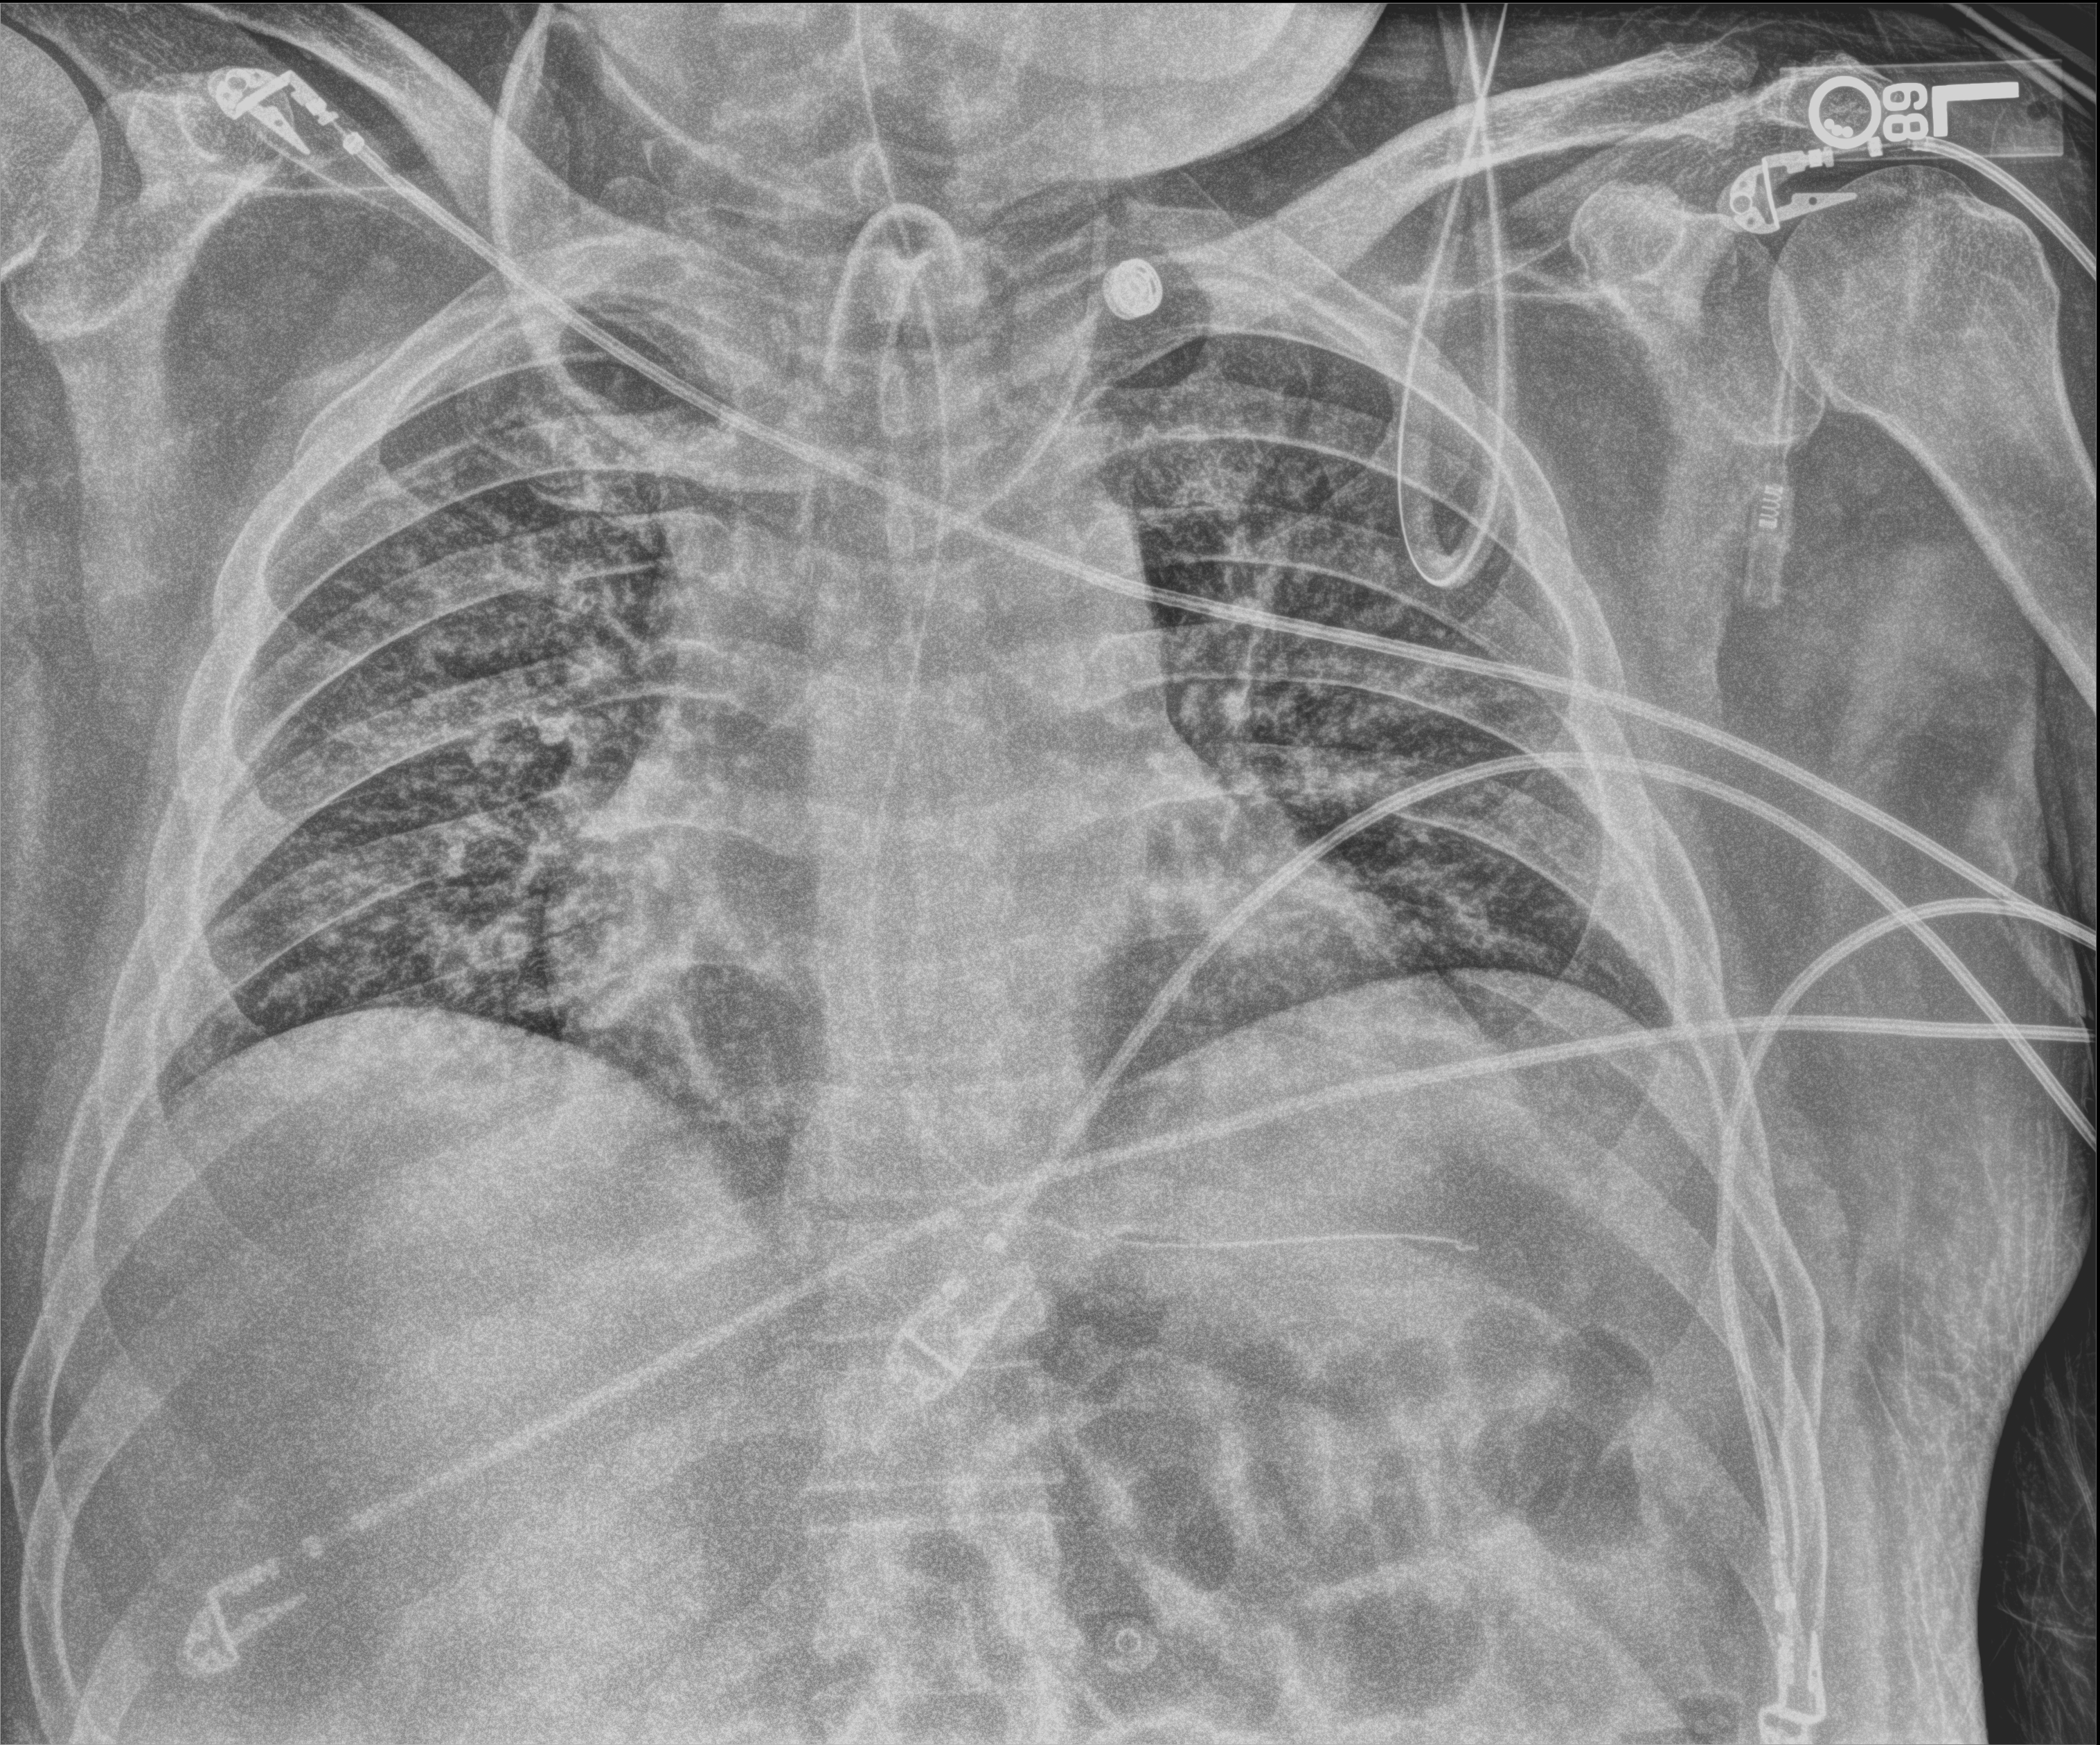
Portable chest radiograph; anteroposterior (AP) projection. Patient hospitalised with COVID-19; male, aged 18–59 years.
Hospital-stay facts (about this admission, not read from this image; timing relative to this image not recorded):
- admitted to intensive care during this hospital stay: yes